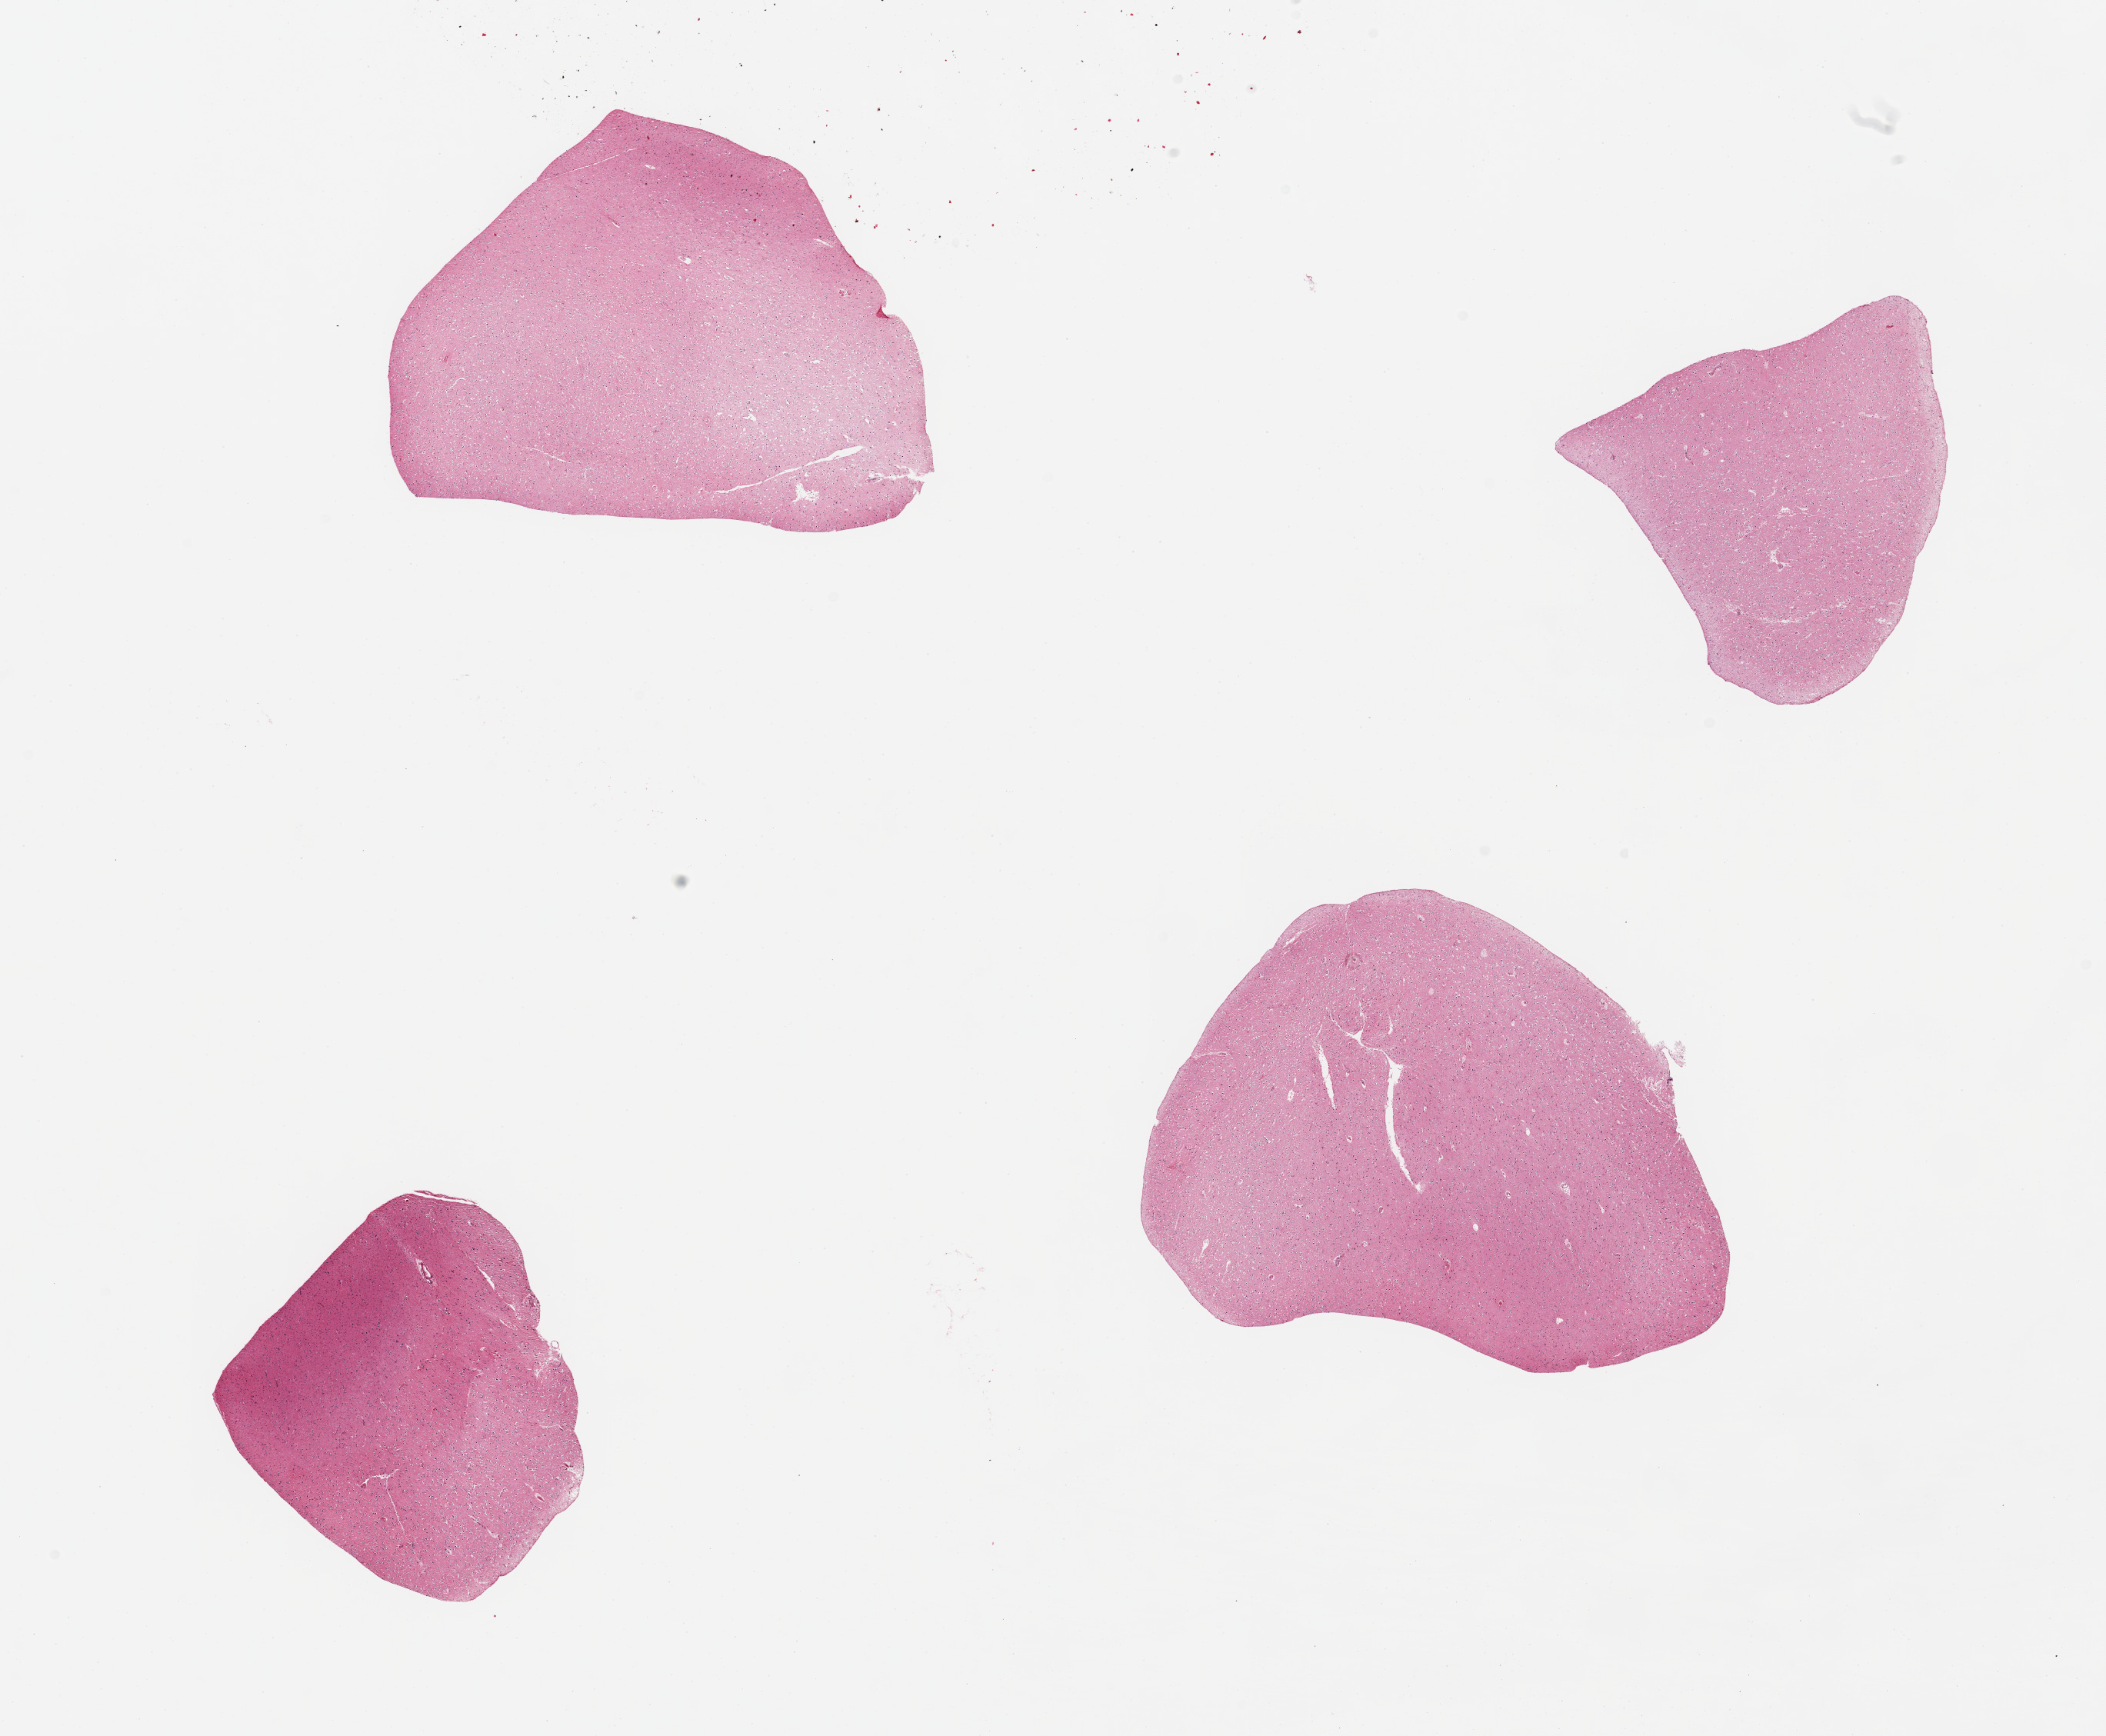
Whole-slide image, H&E stain — whole scanned area (about 21.7 x 17.9 mm) shown as a low-resolution overview, PAXgene-fixed, paraffin-embedded tissue, section of cerebral cortex (target tissue), tissue donor sample. Donor: male.
• pathologist's review note for this sample: 4 pieces, no abnormalities